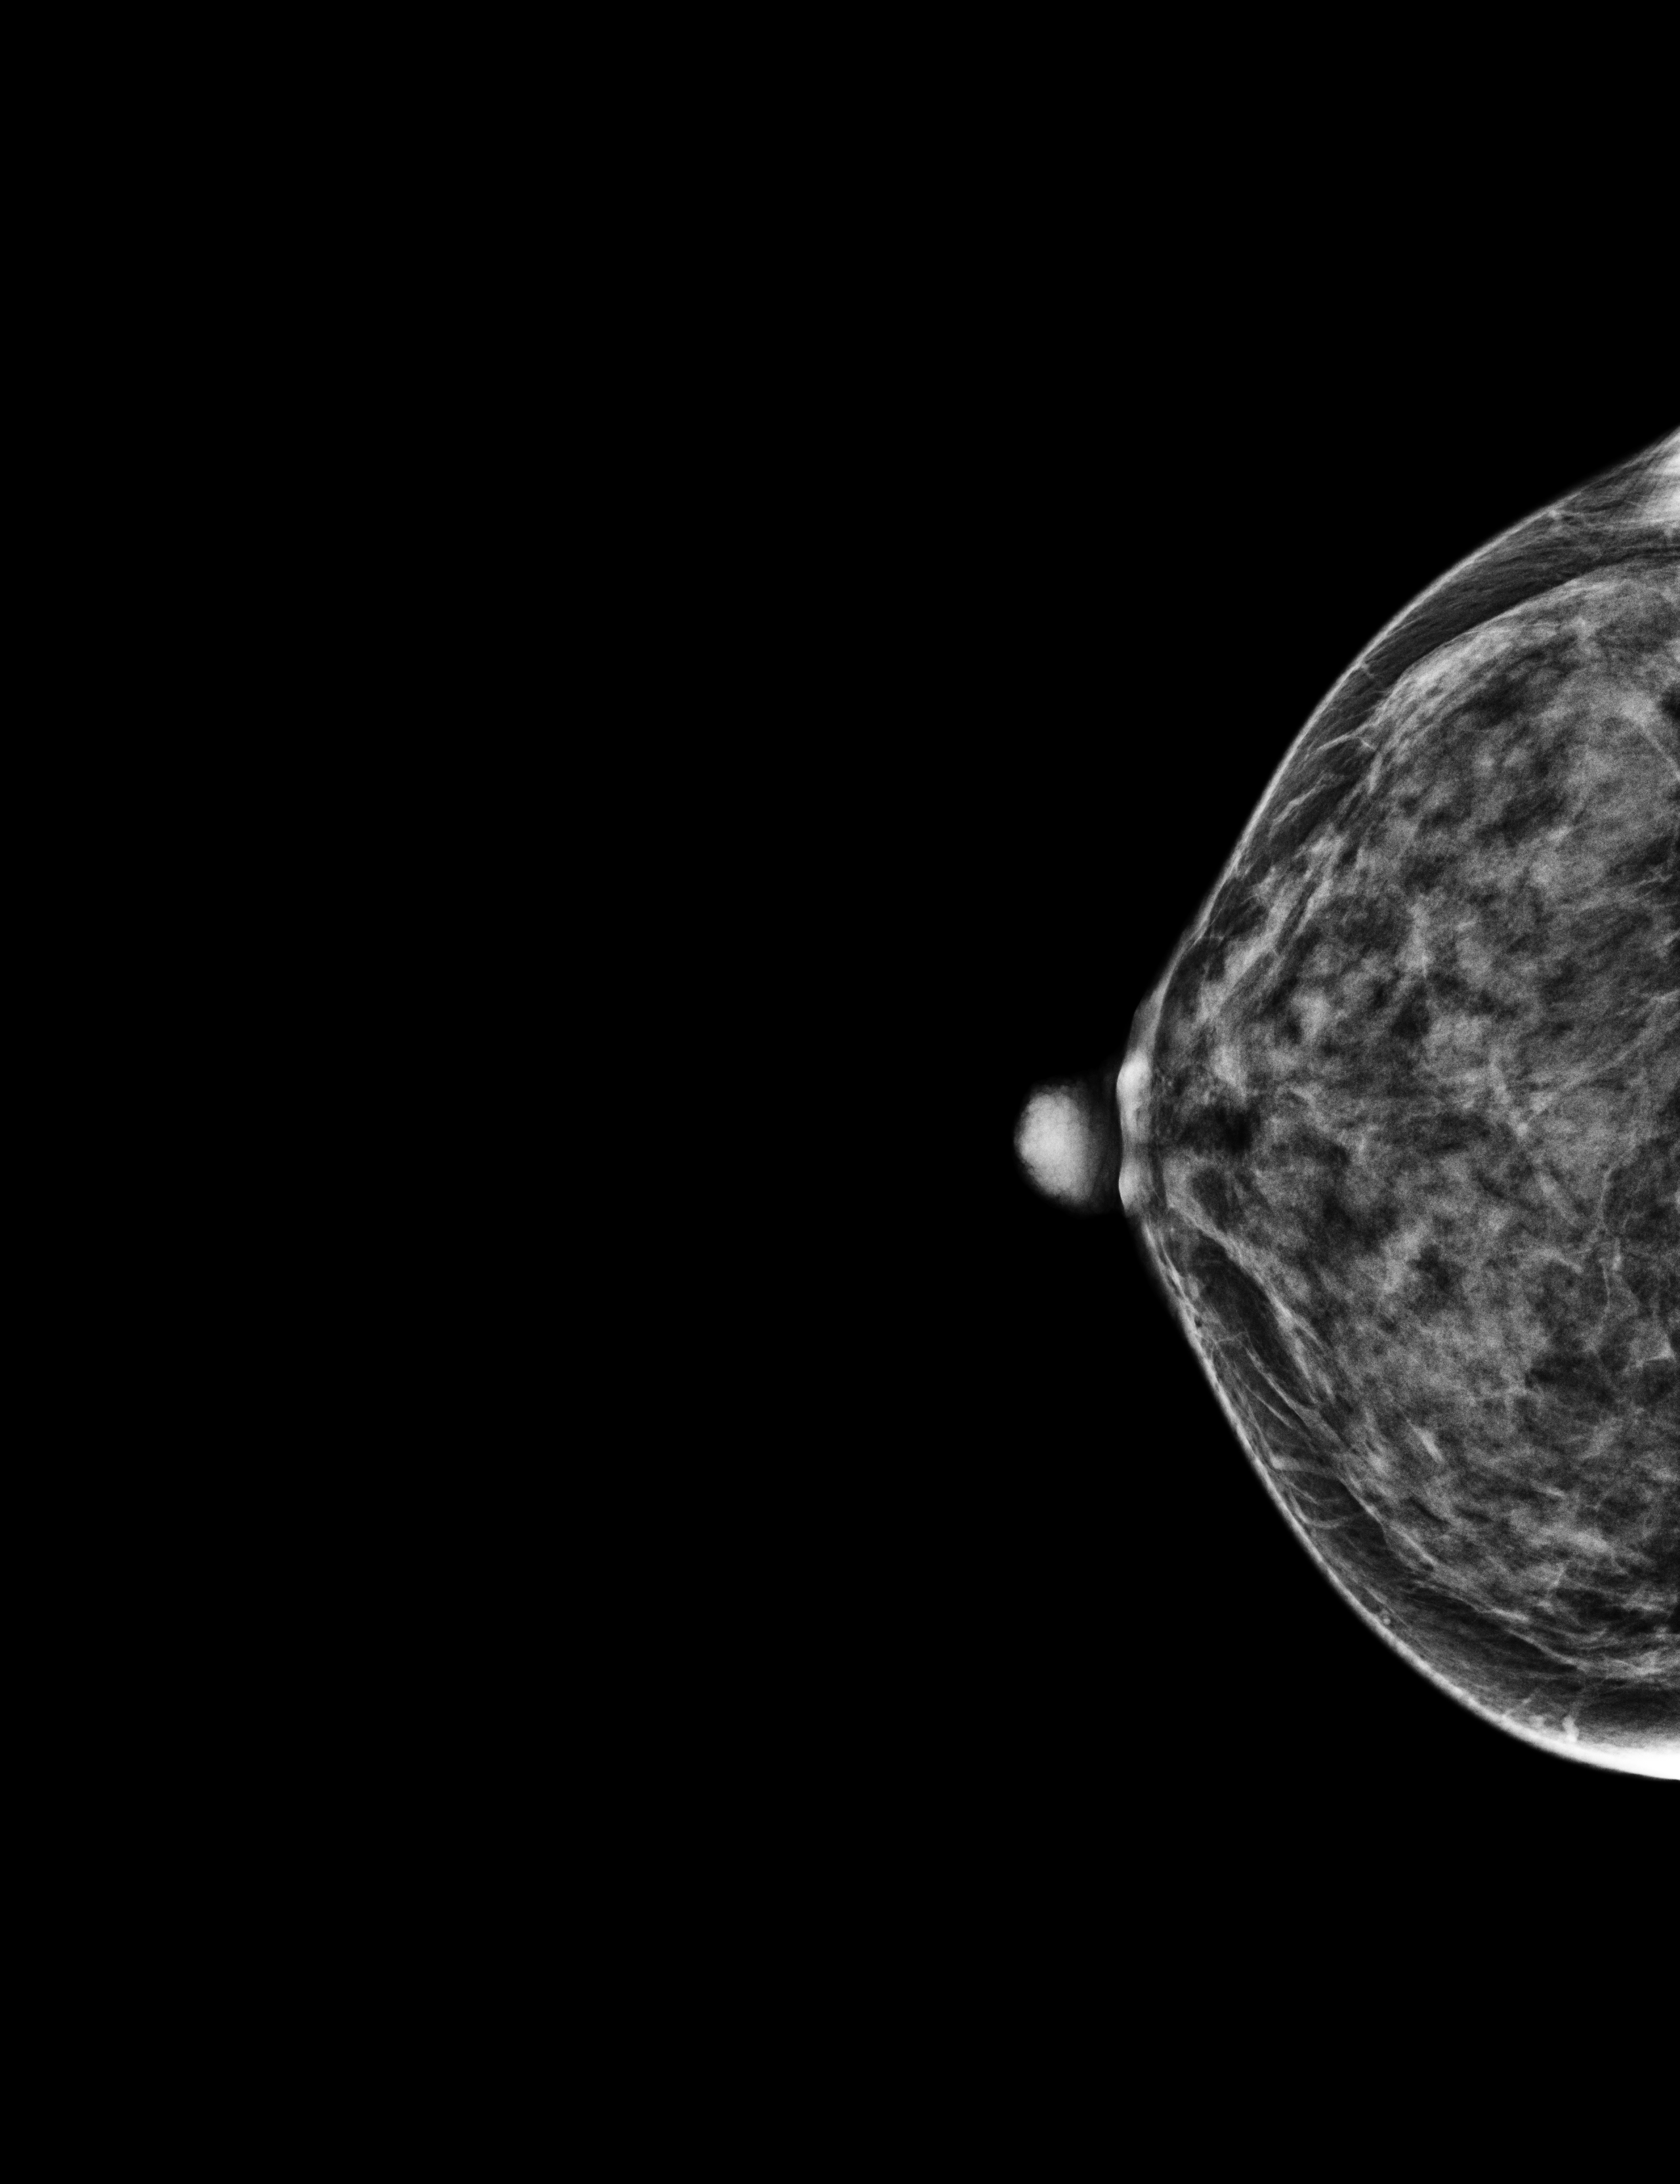
Annual screening mammography examination. Patient aged 43 years (female).
Image type: full-field digital mammogram. Breast: right. Projection: CC view.